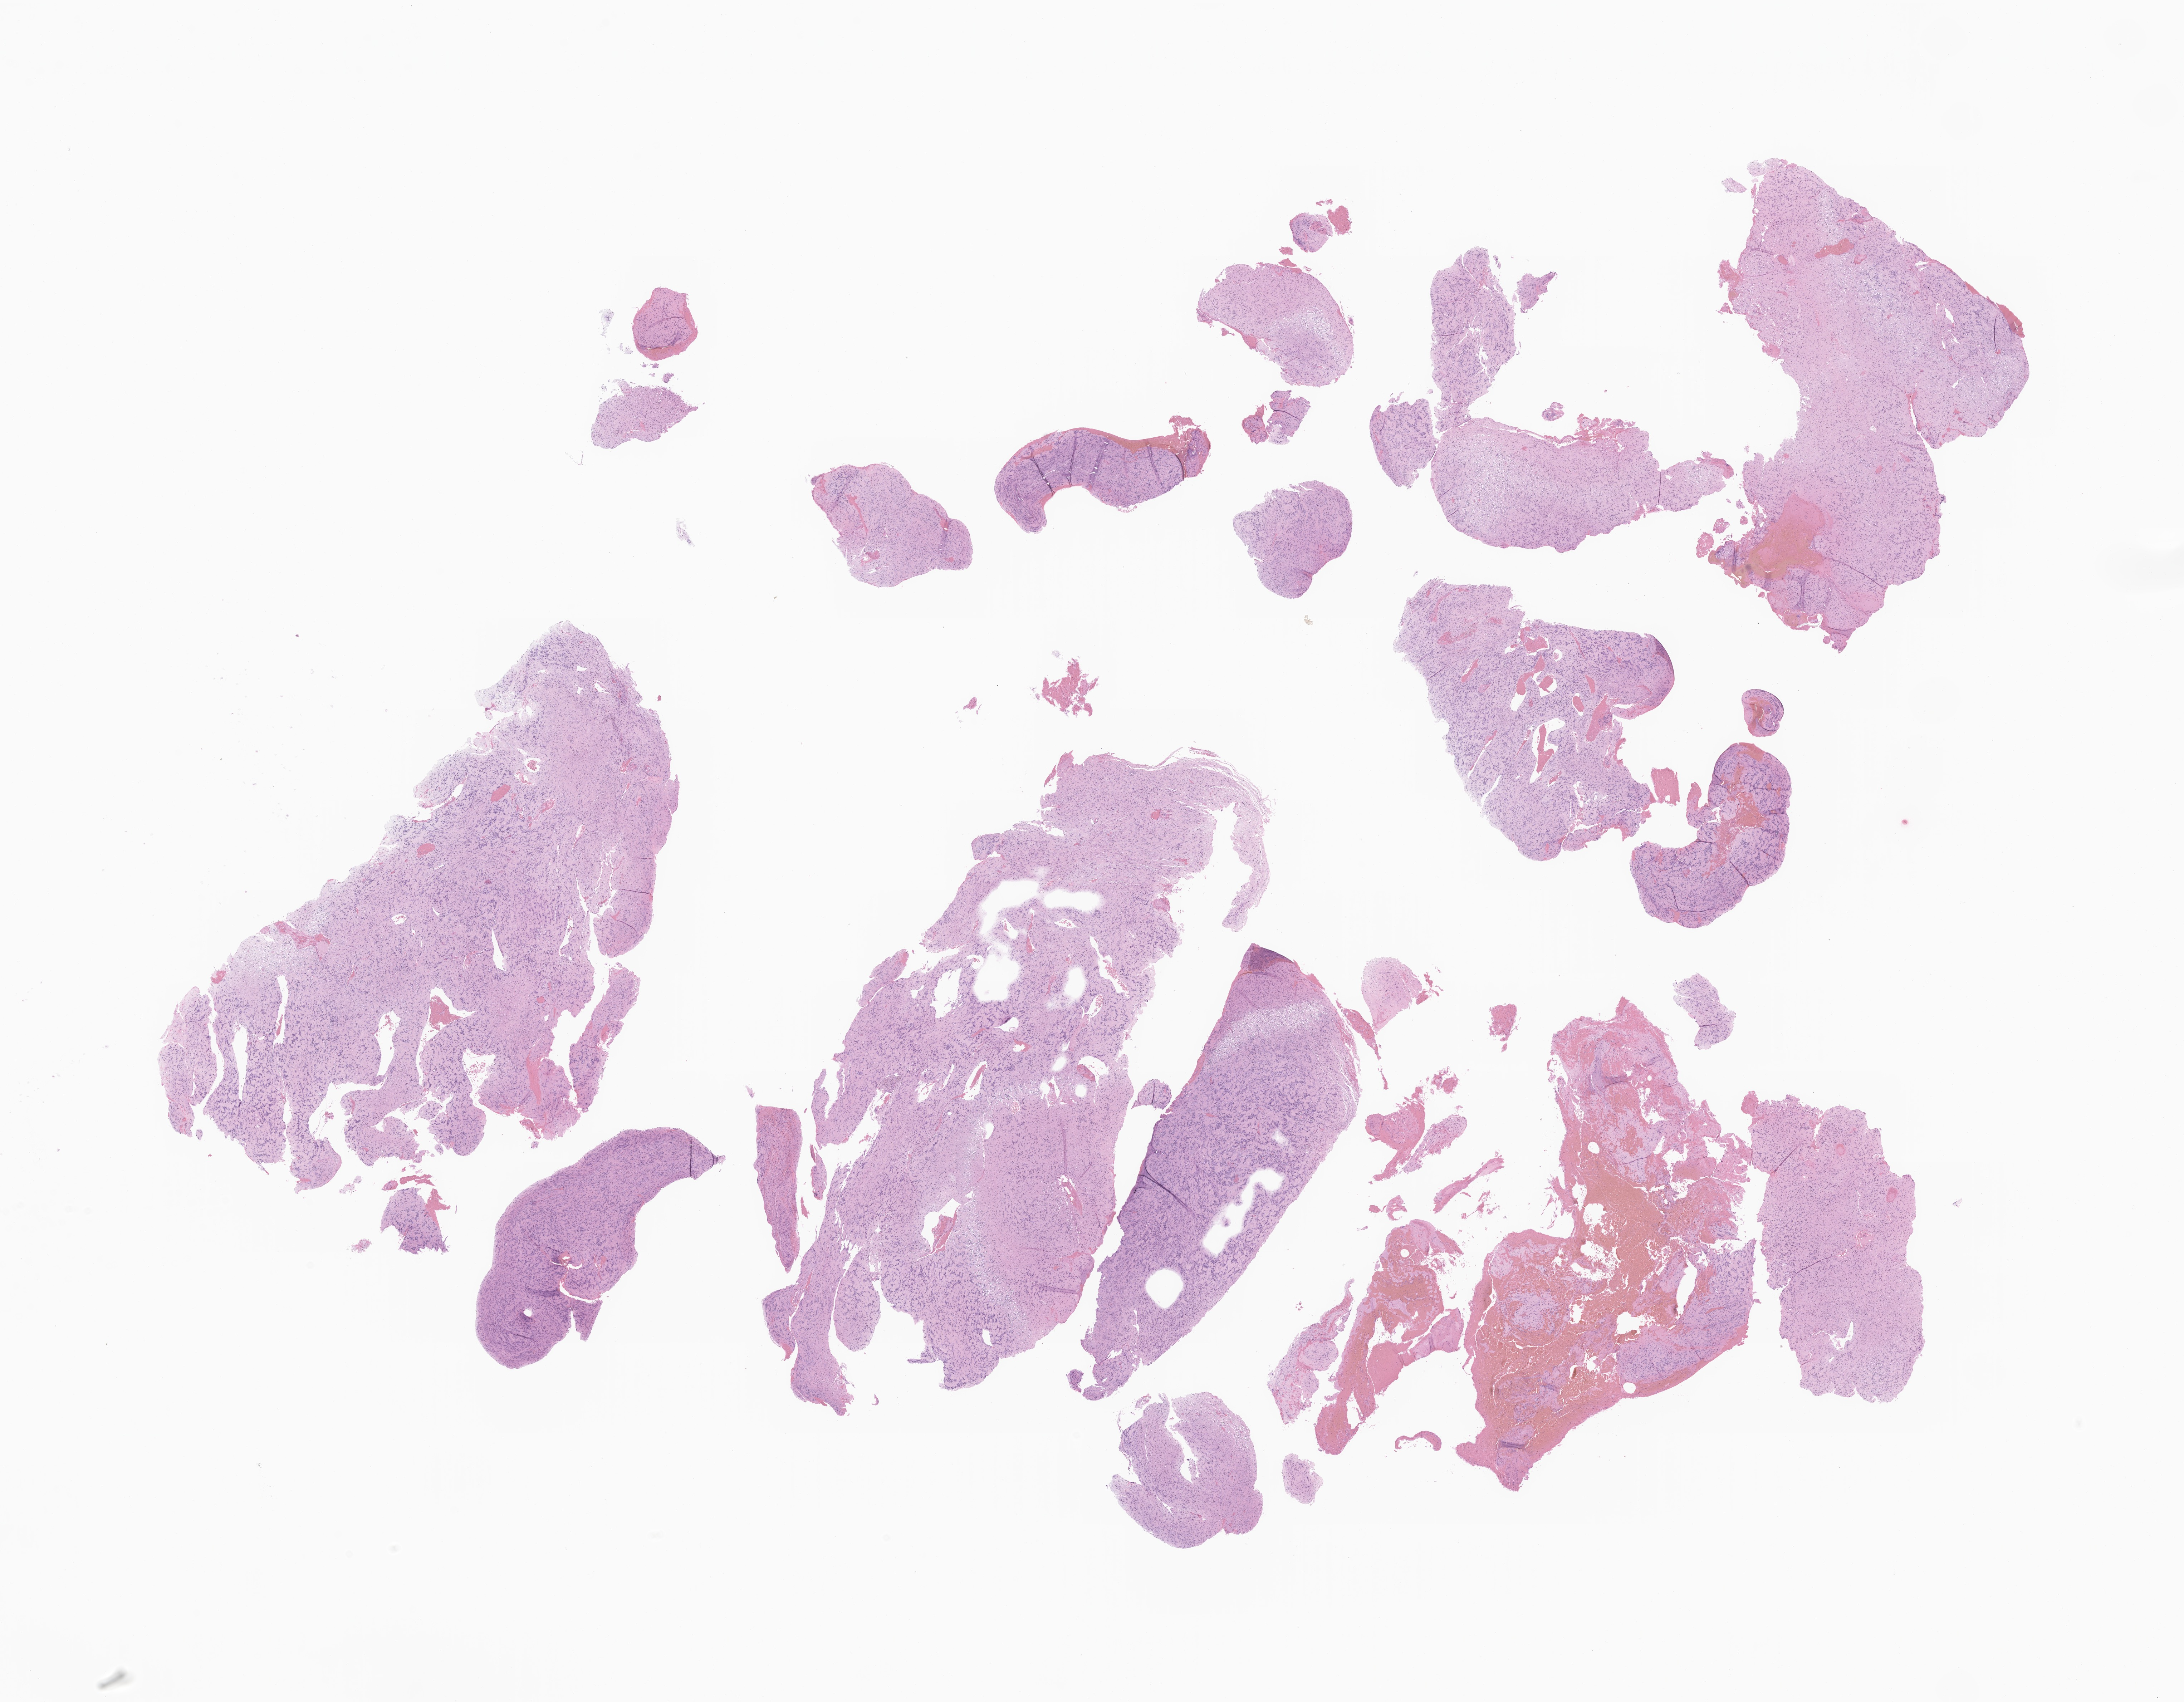
Whole-slide image, haematoxylin and eosin stain of tumor tissue from the brain — a low-resolution overview of the entire scanned area, about 25.7 x 20.1 mm. Formalin-fixed, paraffin-embedded (FFPE) tissue. Patient male; age 196 months (16 years 4 months).
Diagnosis: Schwannoma, NOS.